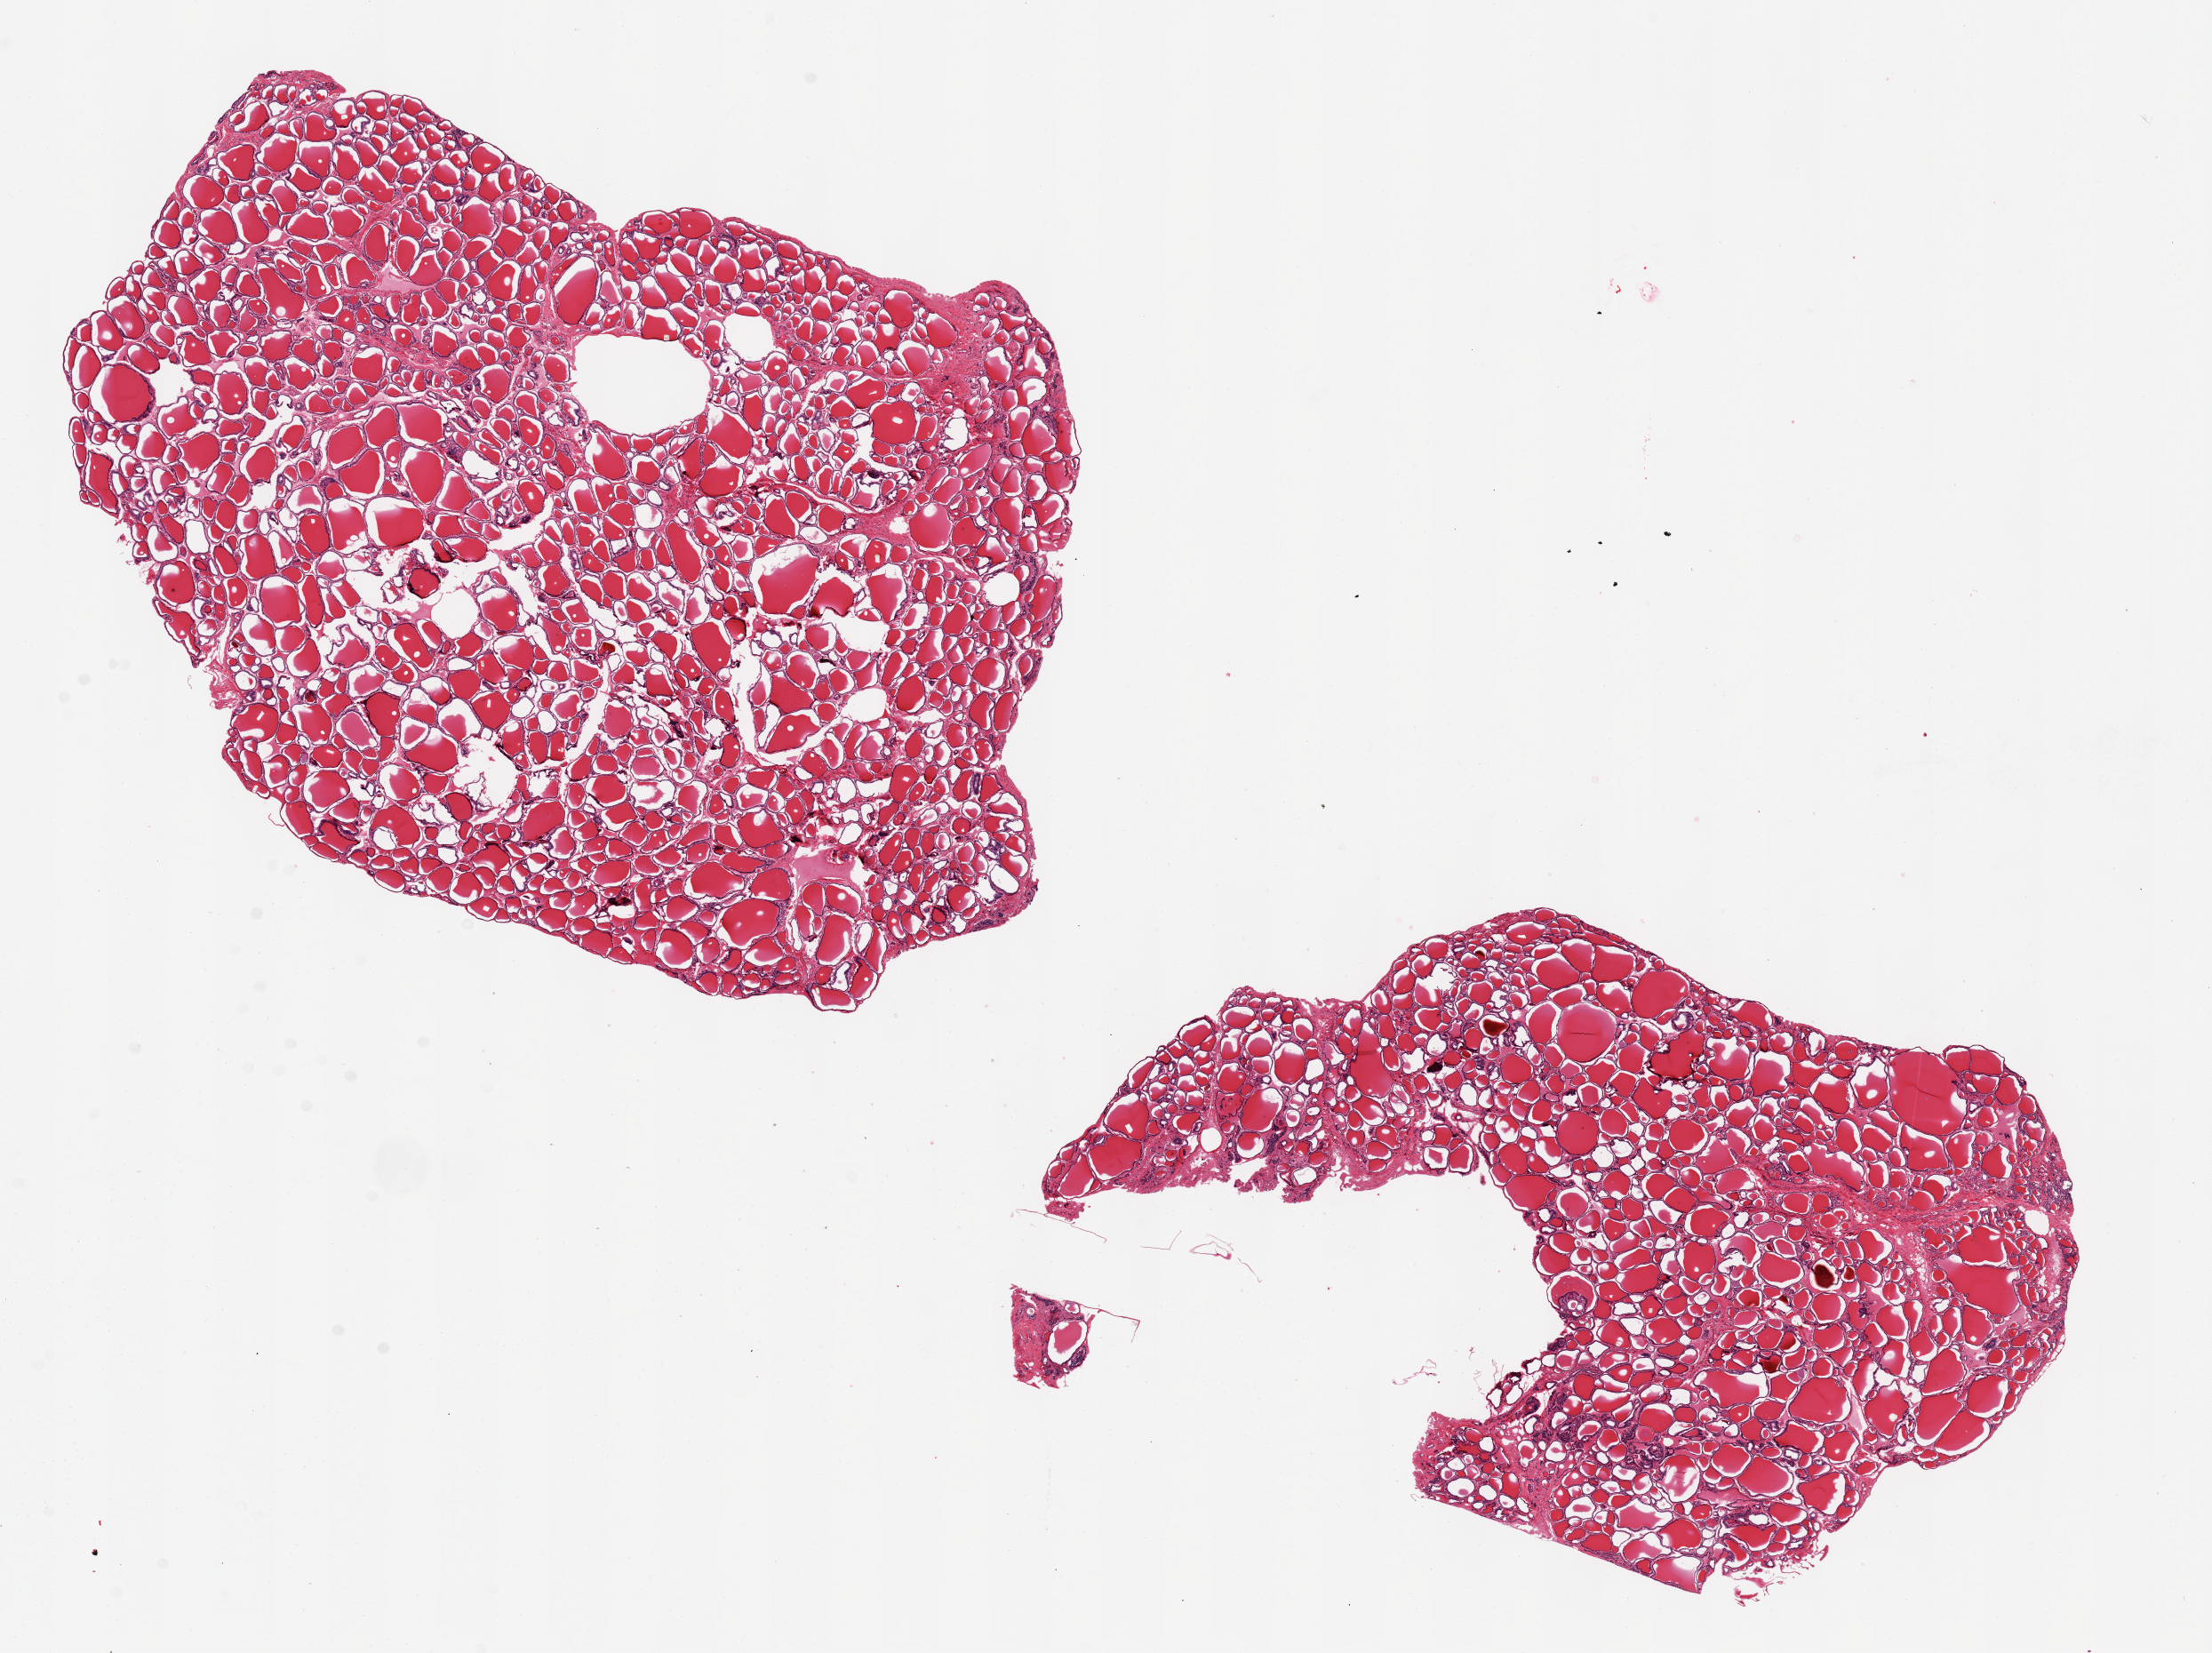
Whole-slide image, haematoxylin and eosin stain, brightfield — a low-resolution overview of the entire scanned area, about 19.7 x 14.7 mm (acquisition: 20x scan), PAXgene-fixed, paraffin-embedded tissue, target tissue: thyroid, tissue donor sample.
• review note (as recorded): 2 pieces, 6.6x8.8 mm & ~6mm